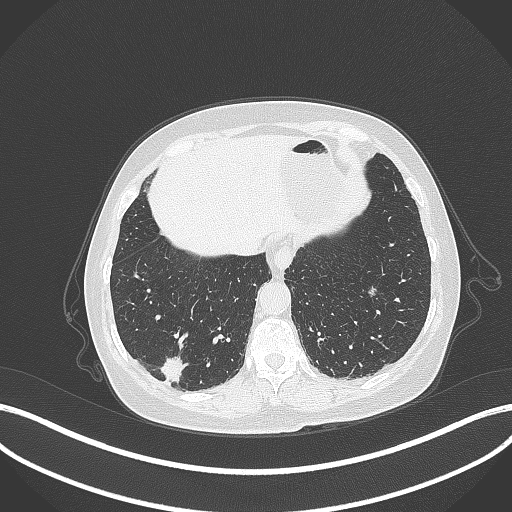
Chest CT, one axial slice. Reconstruction kernel B70f. 120 kVp. Lung window (W 1500 / L -600 HU). 1 mm slice thickness. 512 × 512 image matrix, field of view 400 × 400 mm. Patient: female, 69 years. From the clinical record (not read from this slice): clinical TNM (as recorded): T1b N0 M0; histopathological grade: G2-3.
Annotated regions visible in this slice (bounding box drawn by a radiologist):
- lung tumour (recorded histology: adenocarcinoma): bounding box (x1, y1, x2, y2) in pixels: (157, 350, 187, 388)